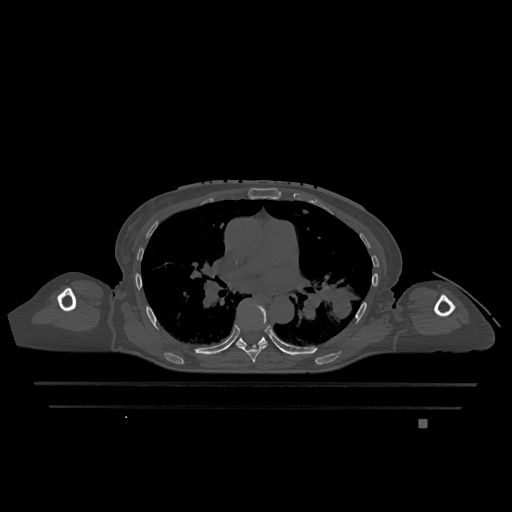
CT including the spine, one axial slice; slice 767 of 1317 in the series (ordered by position); bone window (W 1800 / L 400 HU); 0.5 mm slice thickness; 512 × 512 image matrix, field of view 500 × 500 mm. Female patient, age 74 years. From the clinical record (not read from this slice): primary cancer: lung; vertebrae with lytic lesions (as recorded): T1, T4, T5, T6, L4, L5.
Annotated regions visible in this slice (semi-automatically segmented with operator editing):
- T6 vertebra: bounding box <237,304,269,362> (left, top, right, bottom; pixels)
- T7 vertebra: <236,337,267,346>